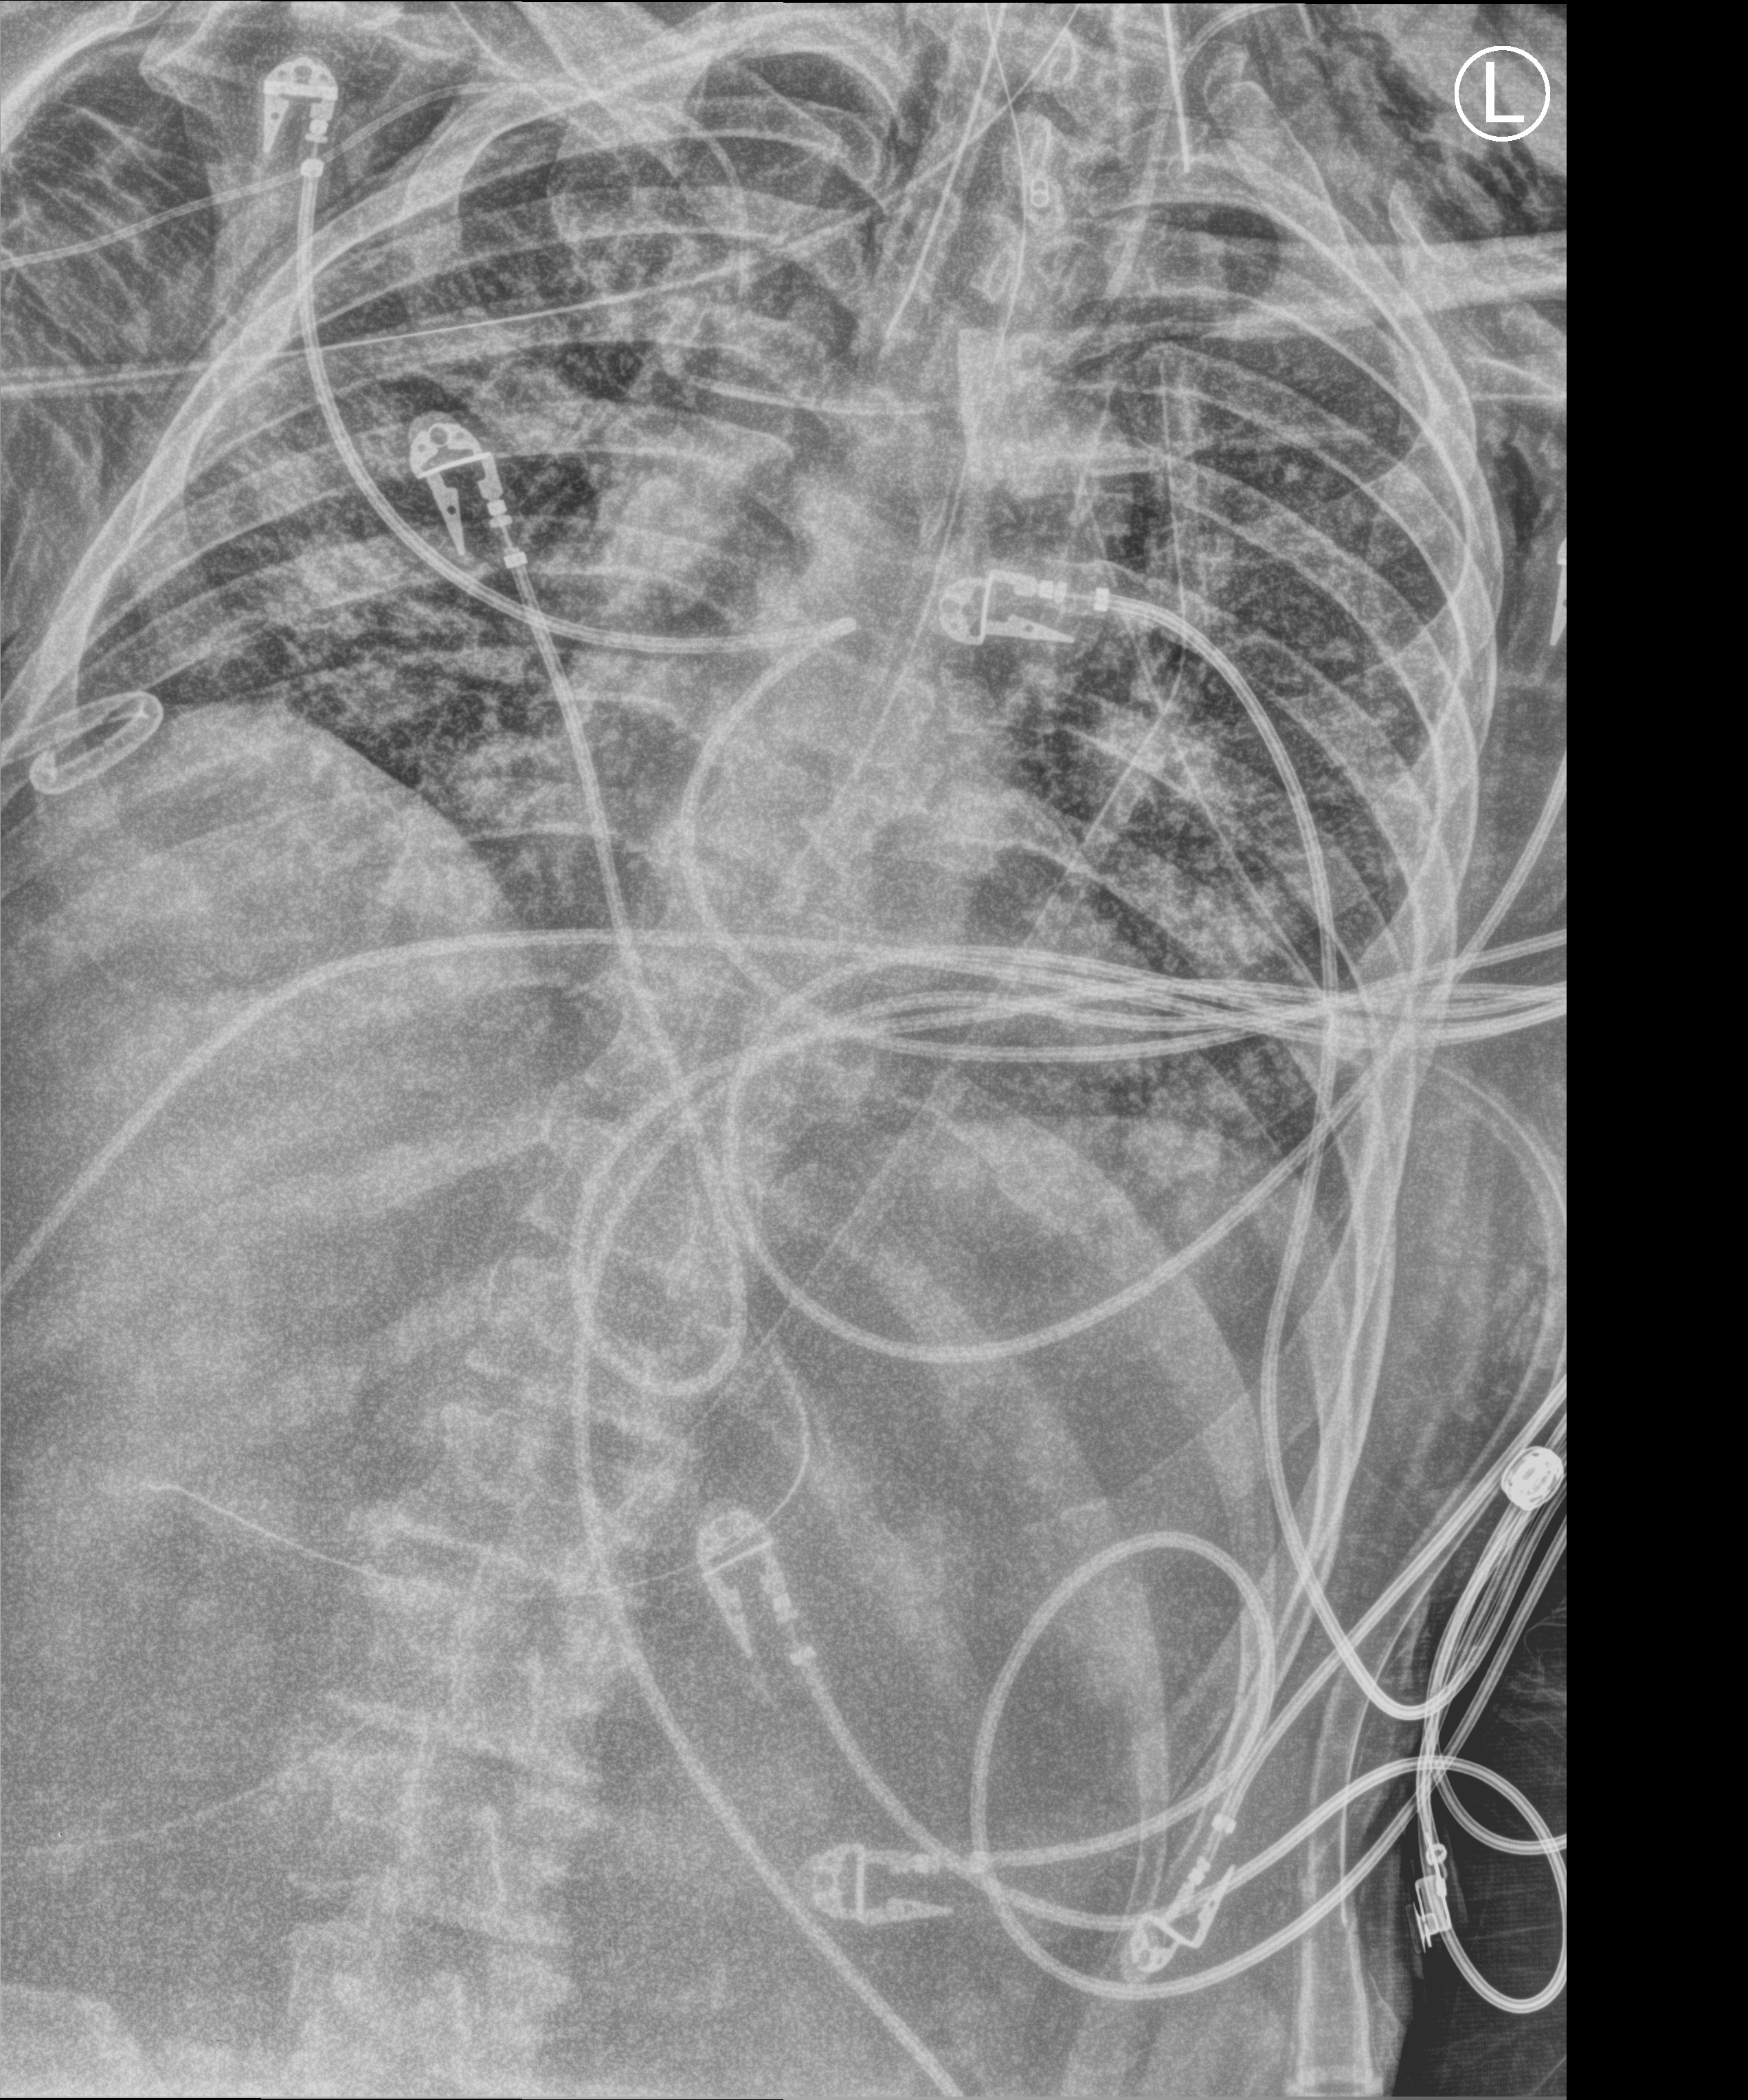
Bedside chest radiograph (computed radiography); anteroposterior (AP) projection. Male patient hospitalised with COVID-19, age 18–59 years.
Admission-level facts for this patient (not findings on this image; timing relative to this image not recorded):
- admitted to intensive care during this hospital stay: yes
- other chronic lung disease (admission record): no